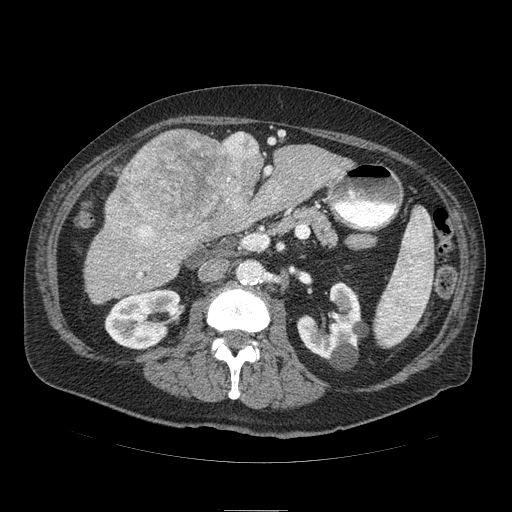
Contrast-enhanced abdominal CT (liver protocol), one axial slice. Slice 35 of 103 in the series (ordered by position). 120 kVp. Soft-tissue window (W 400 / L 40 HU). 2.5 mm slice thickness. 512 × 512 image matrix, field of view 440 × 440 mm. From the clinical record (not read from this slice): diagnosis: hepatocellular carcinoma (patient treated with transarterial chemoembolisation; whether this scan precedes or follows treatment is not stated here); TNM stage (as recorded): Stage-IIIA; Child-Pugh class: B; tumour differentiation: well differentiated; tumour size: 13 cm.
Structures marked on this image (semi-automatic segmentation, software-assisted and operator-edited):
- liver parenchyma outside the tumour (the mass and vessels are separate outlines, so this box may not span the whole liver): bounding box (x1, y1, x2, y2) in pixels: (84, 130, 352, 302)
- mass: (106, 129, 263, 252)
- liver vessels: (138, 167, 271, 278)